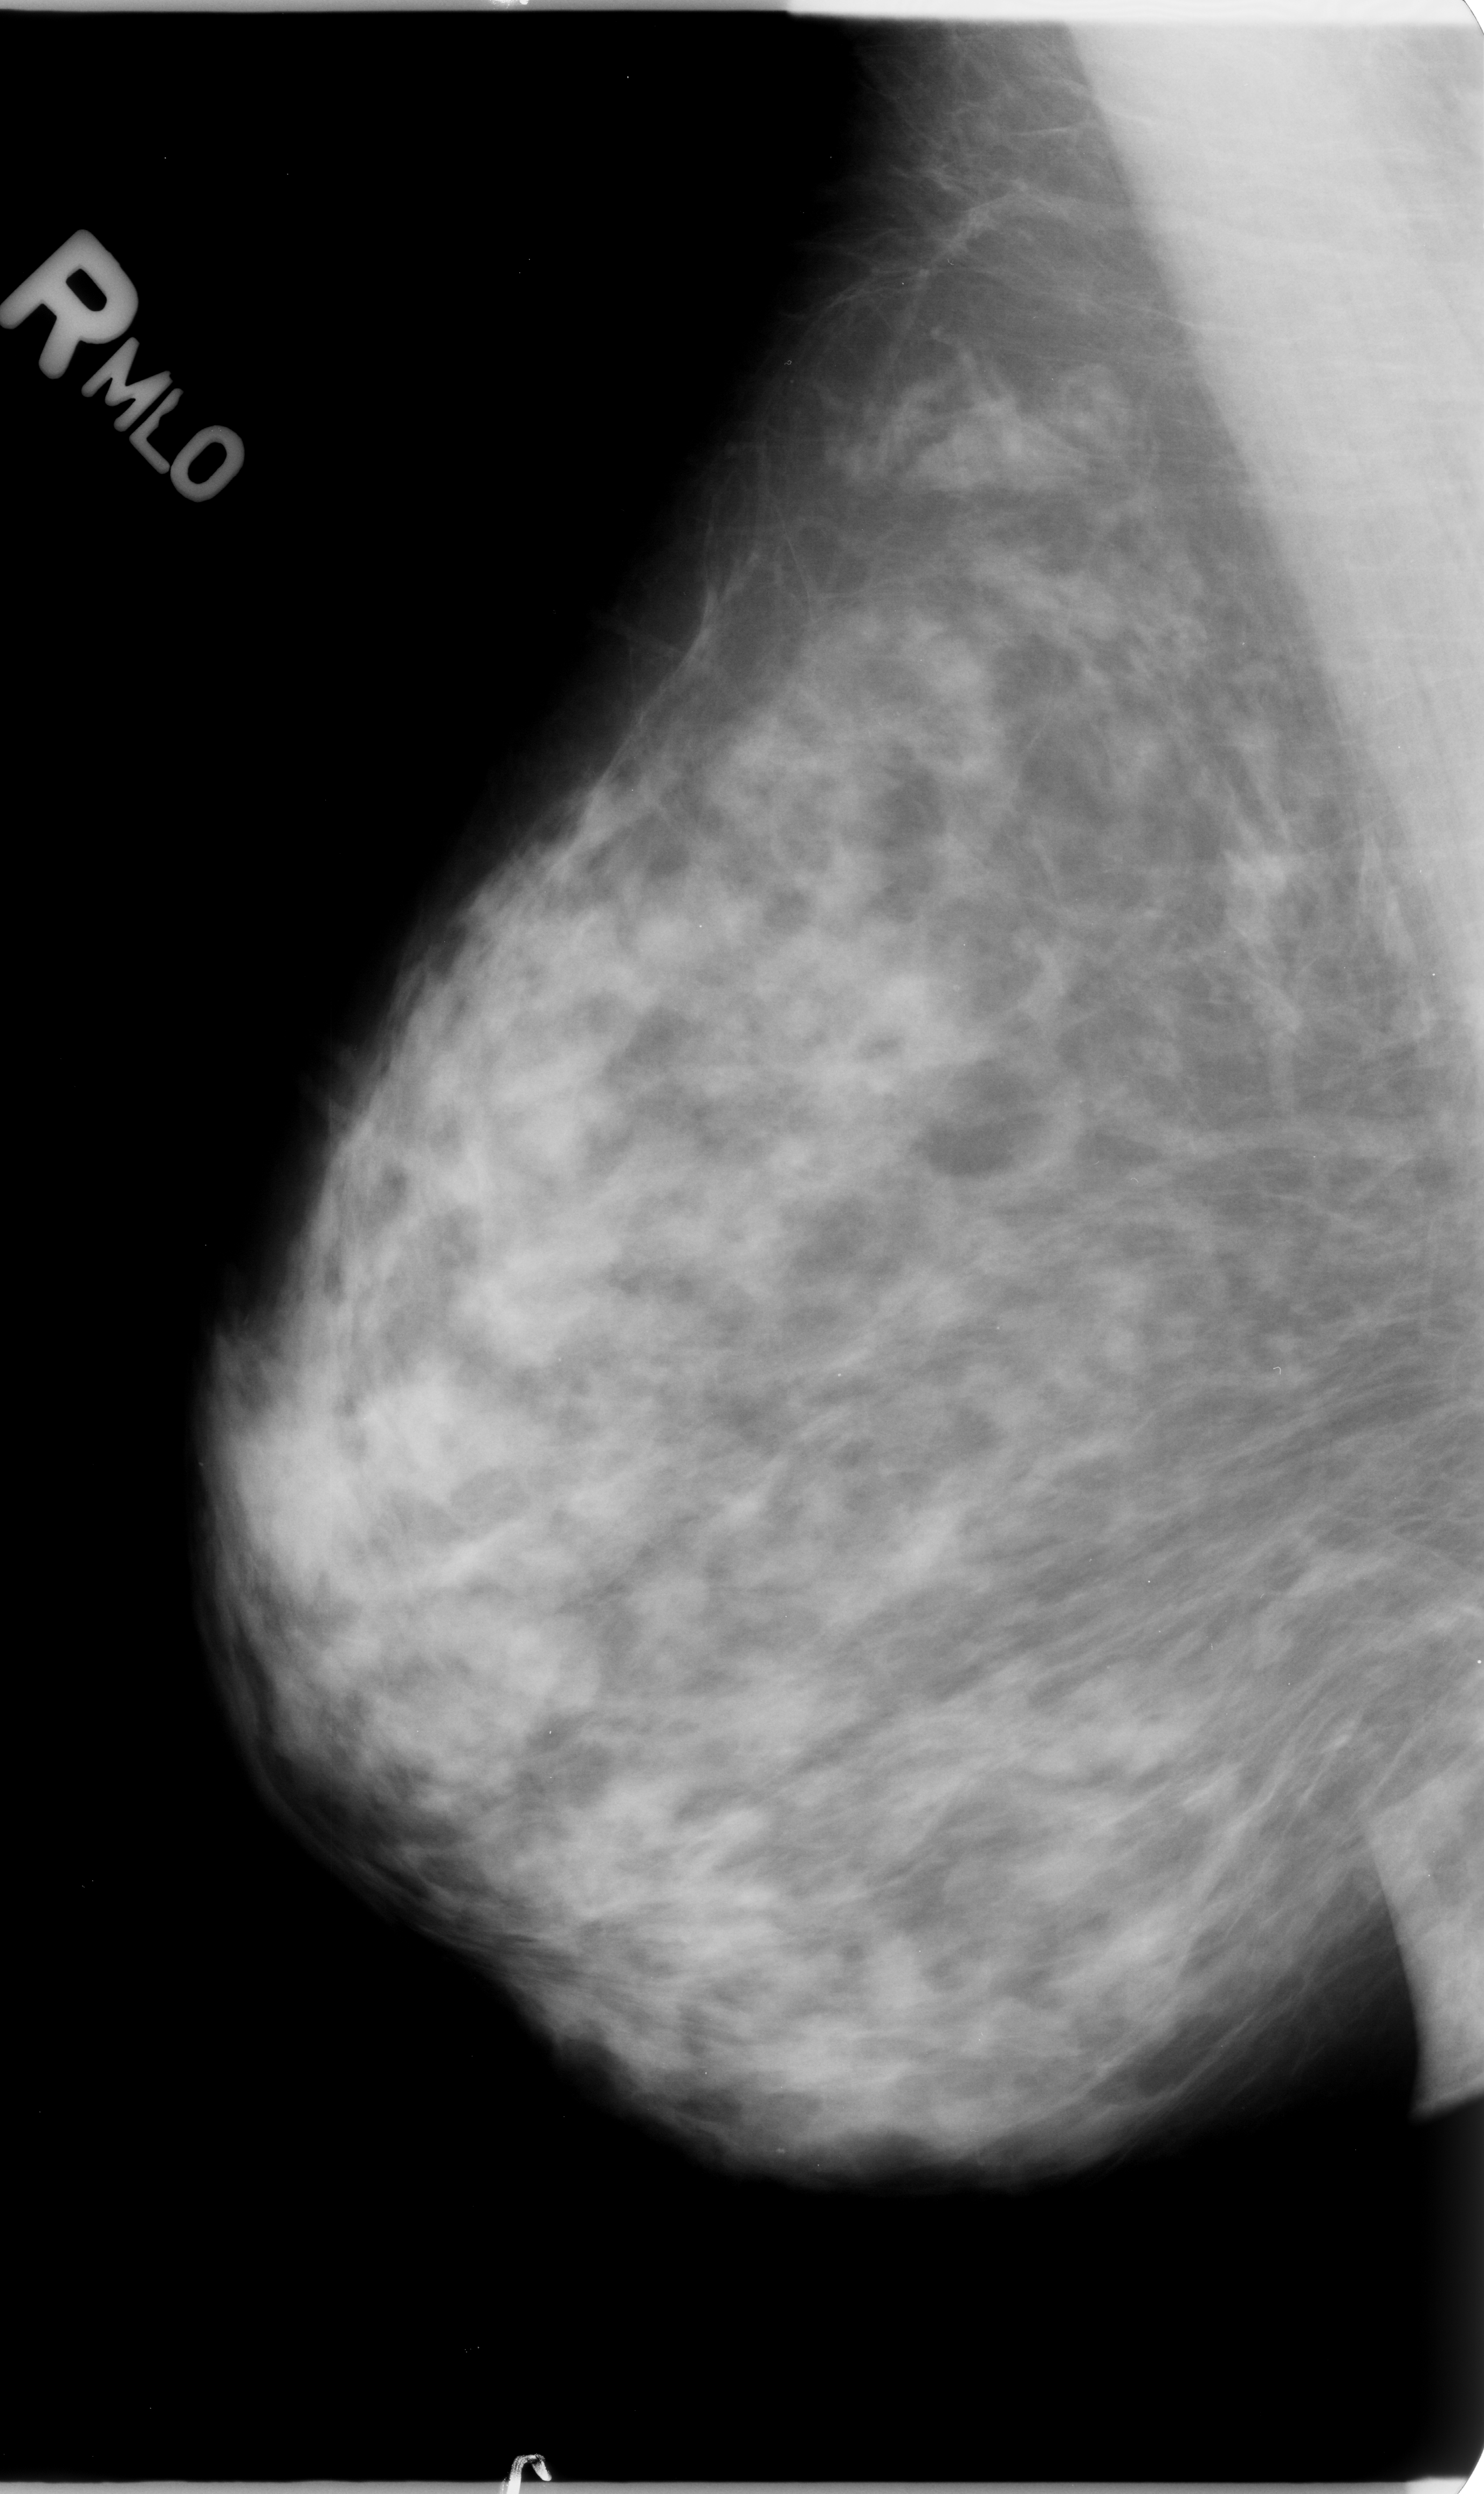
Mammogram (digitized film); right breast; mediolateral oblique (MLO) view; breast composition: heterogeneously dense (BI-RADS density category 3 of 4).
Marked findings (only marked abnormalities are described; nothing is implied about the rest of the image): calcifications, morphology pleomorphic, distribution clustered; BI-RADS assessment category 4; pathology (as recorded): benign.